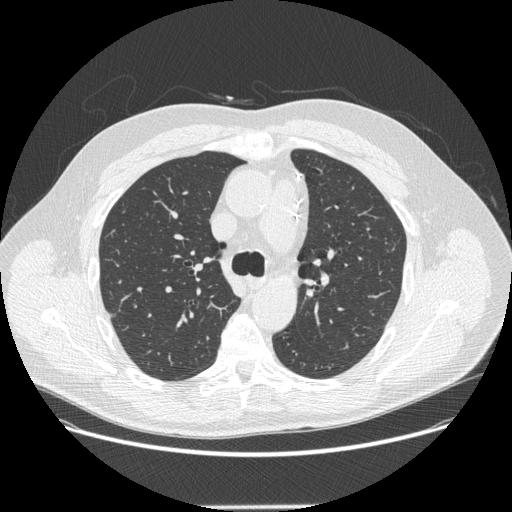
Chest CT (low-dose screening protocol), one axial image, third annual screen, lung window (W 1500 / L -600 HU), 1.25 mm slice thickness, 512 × 512 image matrix. Male, age 62 years at enrolment. Current smoker at enrolment.
• Lesion marked by an expert reader, bounding box [x1, y1, x2, y2] px = [93, 296, 134, 339].
• Reader record for this screening exam (exam-level; its link to the box is not recorded): non-calcified nodule or mass ≥4 mm, right upper lobe, 12 × 11 mm, smooth margins, soft tissue attenuation, pre-existing on the prior screen: yes; interval growth: yes.
• Later outcome: lung cancer diagnosed 112 days after this screen — adenocarcinoma, NOS, right upper lobe, moderately differentiated (G2), stage IA (AJCC 6th edition), 12 mm at pathology.